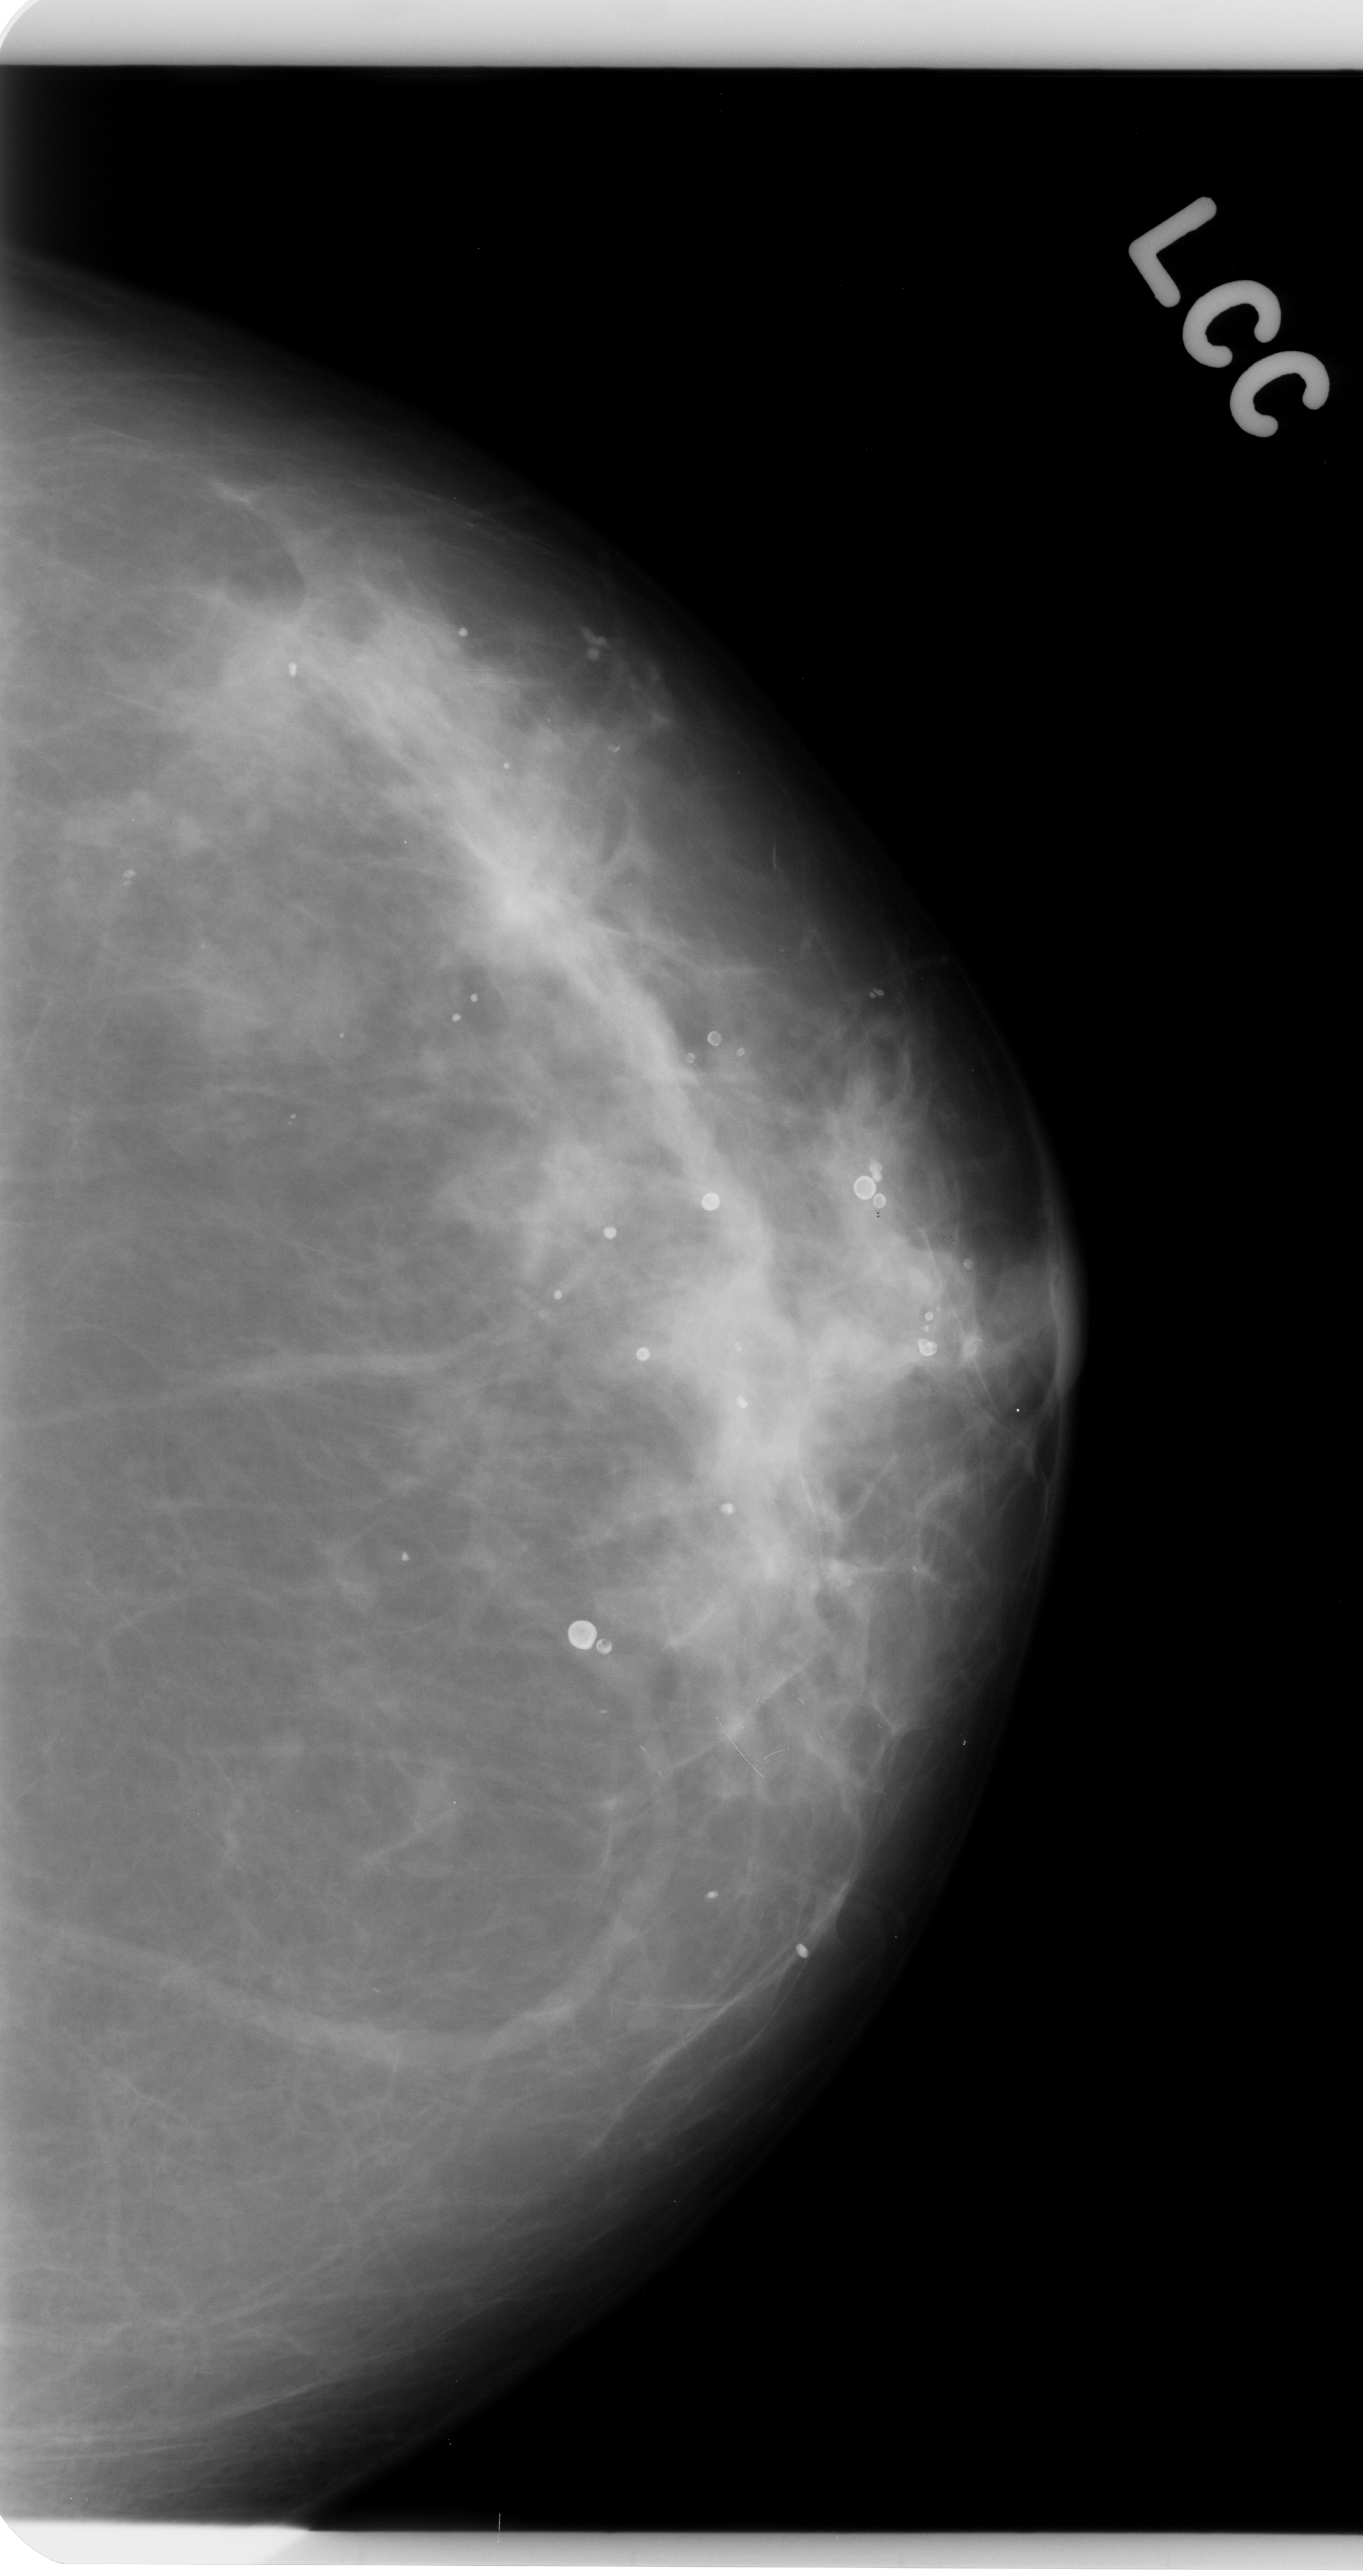
Mammogram (digitized film); left breast; craniocaudal (CC) view; BI-RADS breast density category 2 (scale 1–4).
Marked abnormality: mass, shape architectural distortion, margins spiculated; BI-RADS assessment category 4; subtlety rating 5 on a 1 (subtle) to 5 (obvious) scale; pathology result (as recorded, not read from the image): benign.